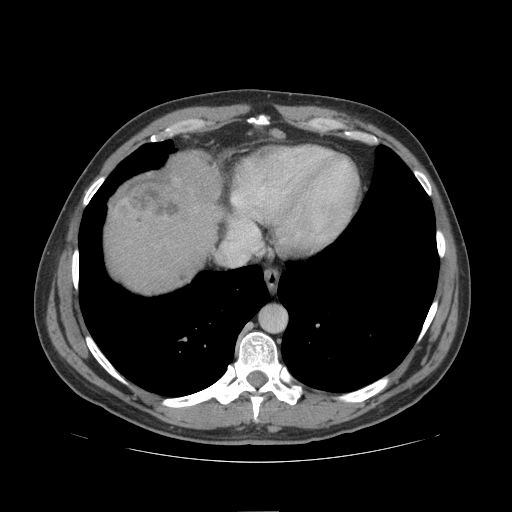
Contrast-enhanced abdominal CT (liver protocol), one axial slice. Slice 93 of 109 in the series (ordered by position). Soft-tissue window (W 400 / L 40 HU). 512 × 512 image matrix. Case-level facts recorded for this patient, not image findings: diagnosis: hepatocellular carcinoma (patient treated with transarterial chemoembolisation; whether this scan precedes or follows treatment is not stated here); TNM stage (as recorded): Stage-IIIB; Child-Pugh class: A; tumour nodularity: multinodular.
Annotated regions visible in this slice (semi-automatic segmentation, software-assisted and operator-edited):
- liver parenchyma outside the tumour (the mass and vessels are separate outlines, so this box may not span the whole liver): bounding box [x1, y1, x2, y2] px = [104, 152, 224, 292]
- mass: [129, 152, 220, 226]